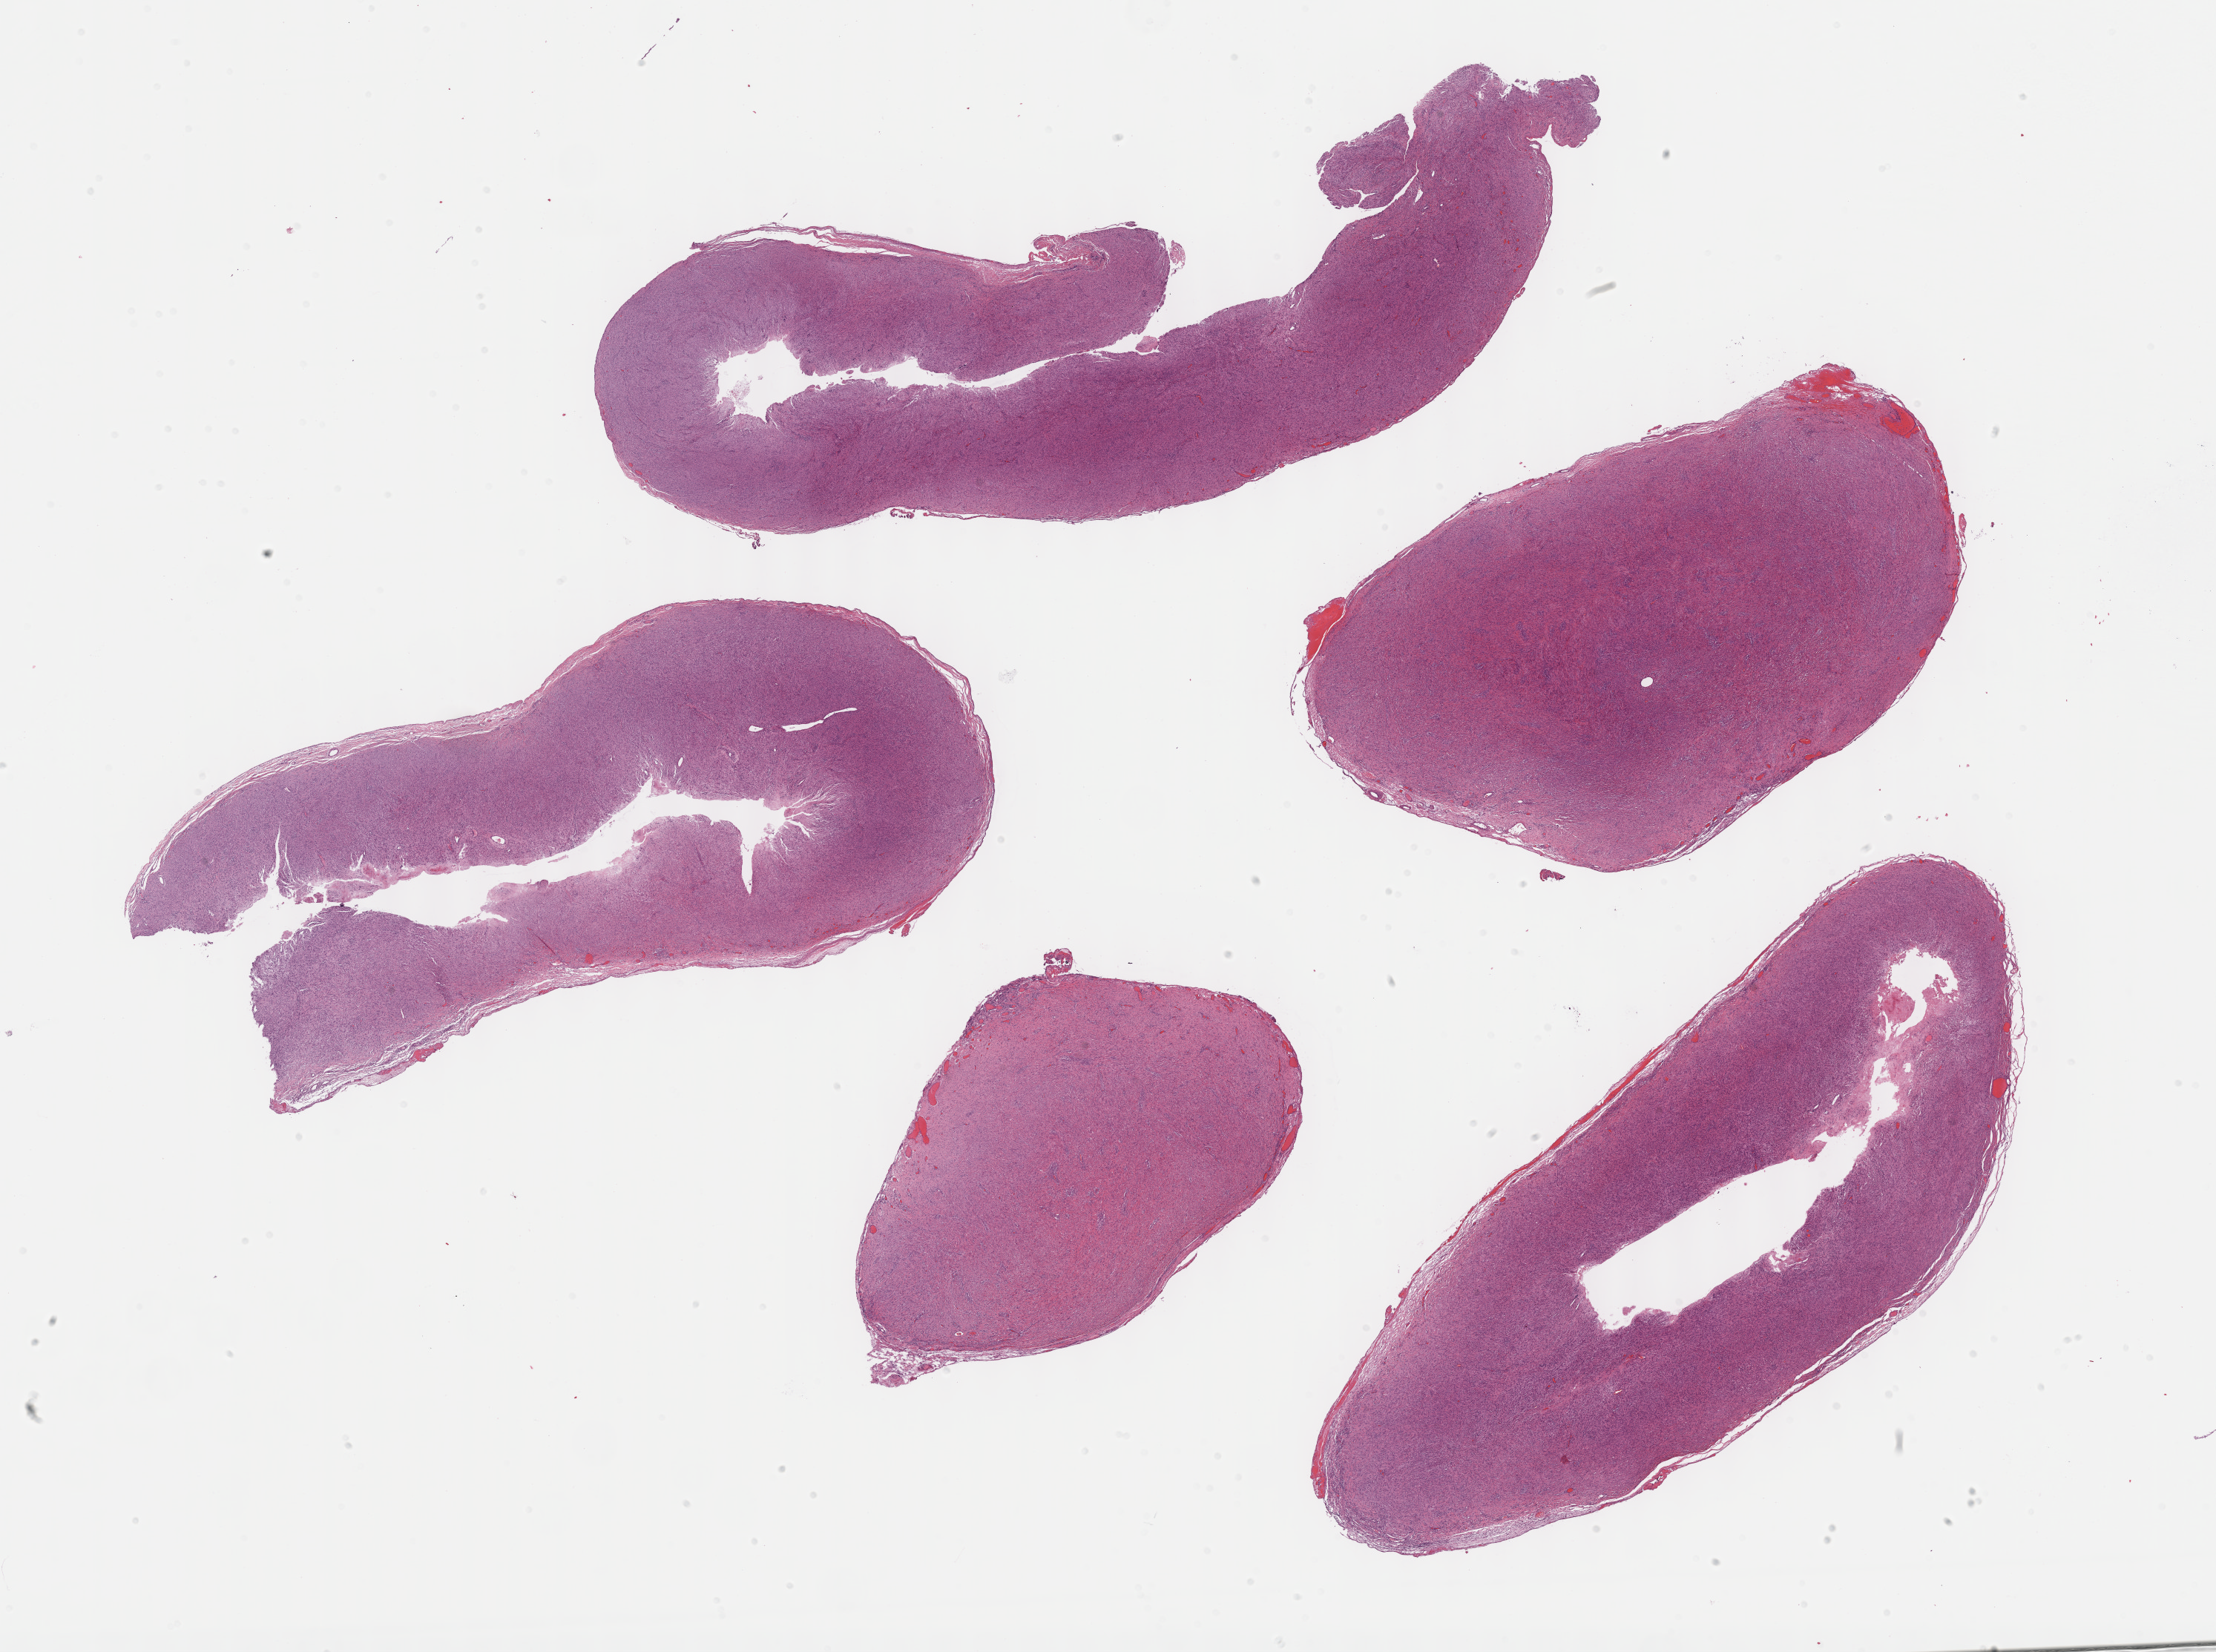
Digitized H&E-stained tissue section (whole slide) — a low-resolution overview of the entire scanned area, about 24.2 x 18.0 mm (from a 40x scan), formalin-fixed paraffin-embedded (FFPE) diagnostic section, meninges, primary tumour sample. Patient: female, age at initial diagnosis 62 years.
Histologic diagnosis: Malignant peripheral nerve sheath tumor (spinal meninges).